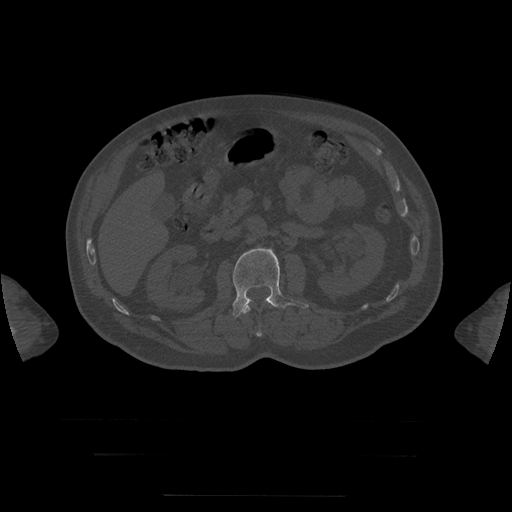
CT including the spine, one axial slice. Position 28 of 397 along the scan axis. Reconstruction kernel STANDARD. Bone window (W 1800 / L 400 HU). 1.25 mm slice thickness. 512 × 512 image matrix. Patient age 73 years. From the clinical record (not read from this slice): primary cancer: prostate.
Annotated regions visible in this slice (semi-automatic segmentation, software-assisted and operator-edited):
- L1 vertebra: box from (x=243, y=301) to (x=269, y=337) px